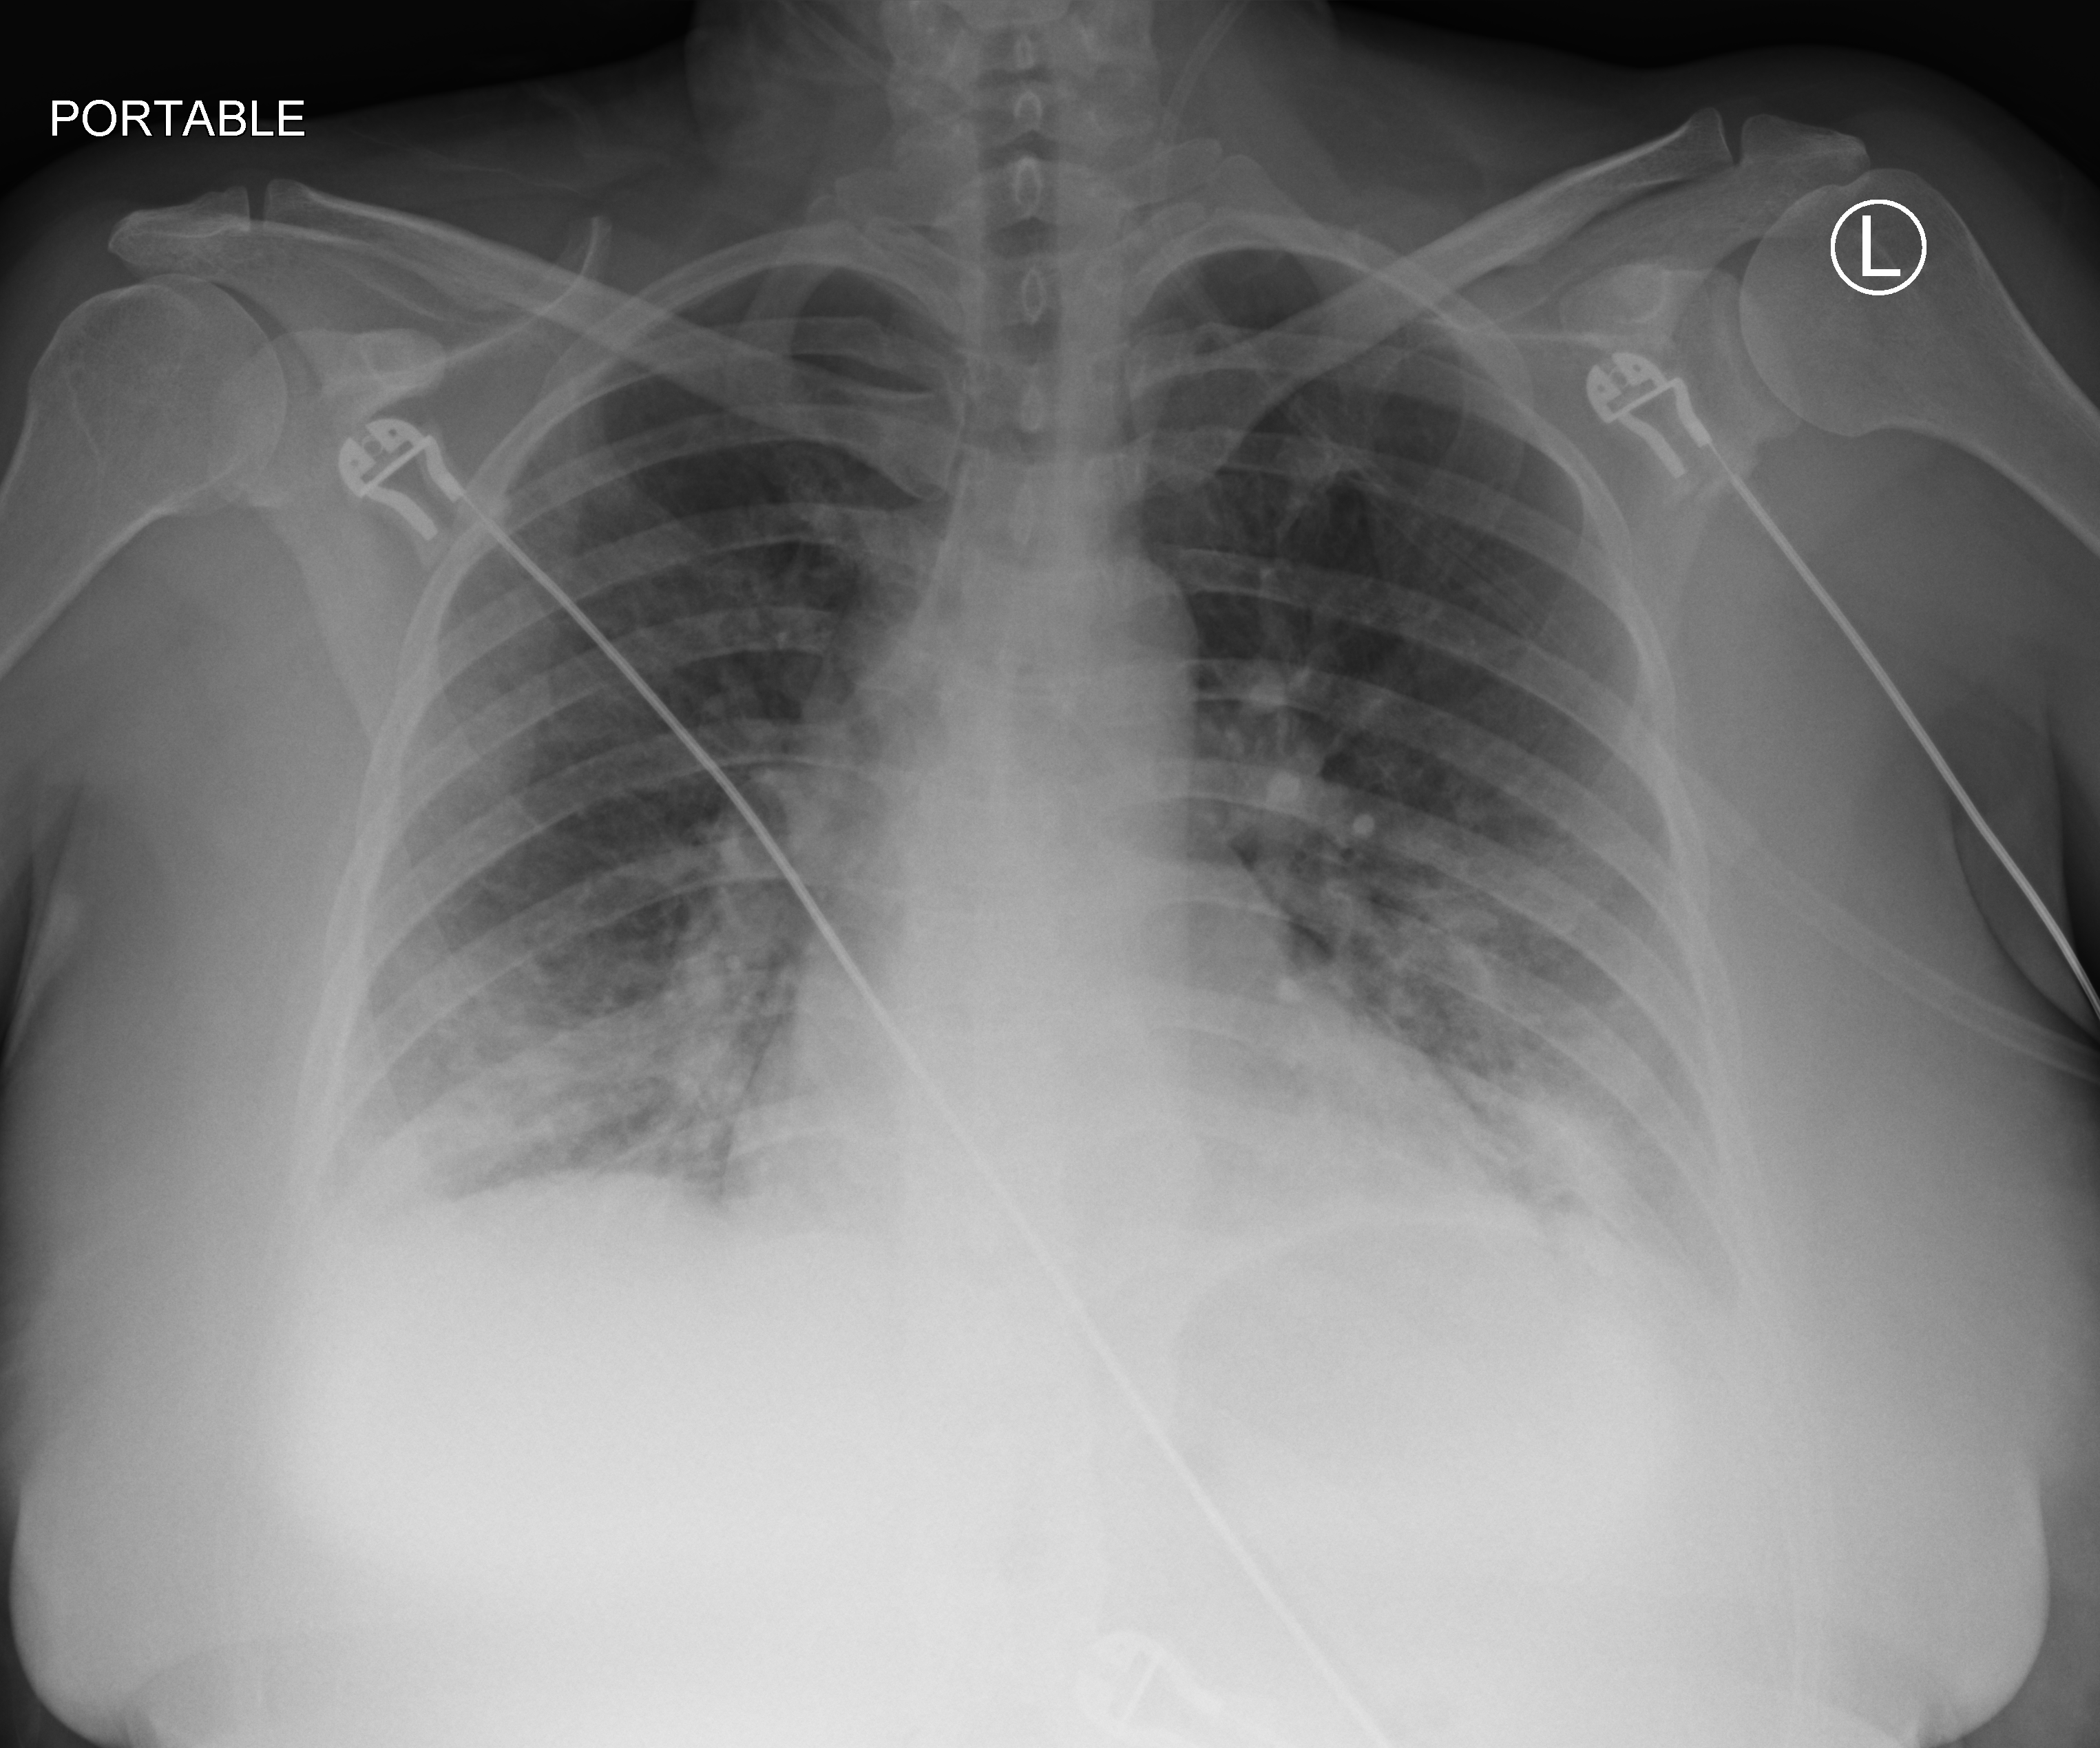
Bedside chest radiograph (computed radiography); anteroposterior (AP) projection. Female patient hospitalised with COVID-19, age 18–59 years.
Hospital-stay facts (about this admission, not read from this image; timing relative to this image not recorded): mechanically ventilated during this hospital stay: no; admitted to intensive care during this hospital stay: no.